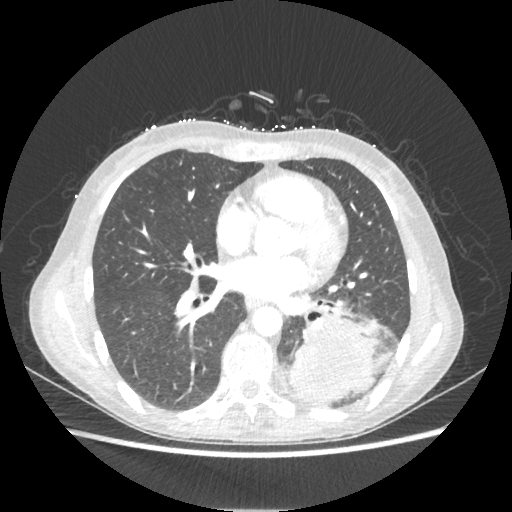
Chest CT, one axial slice. Slice 102 of 221 in the series (ordered by position). Reconstruction kernel STANDARD. 80 kVp. Lung window (W 1500 / L -600 HU). 1.25 mm slice thickness. 512 × 512 image matrix, field of view 360 × 360 mm. Female patient, age 53 years. Case-level facts recorded for this patient, not image findings: clinical TNM (as recorded): T3 N0 M0.
Annotated regions visible in this slice (bounding box drawn by a radiologist):
- lung tumour (recorded histology: adenocarcinoma): bounding box [x1, y1, x2, y2] px = [288, 316, 377, 404]